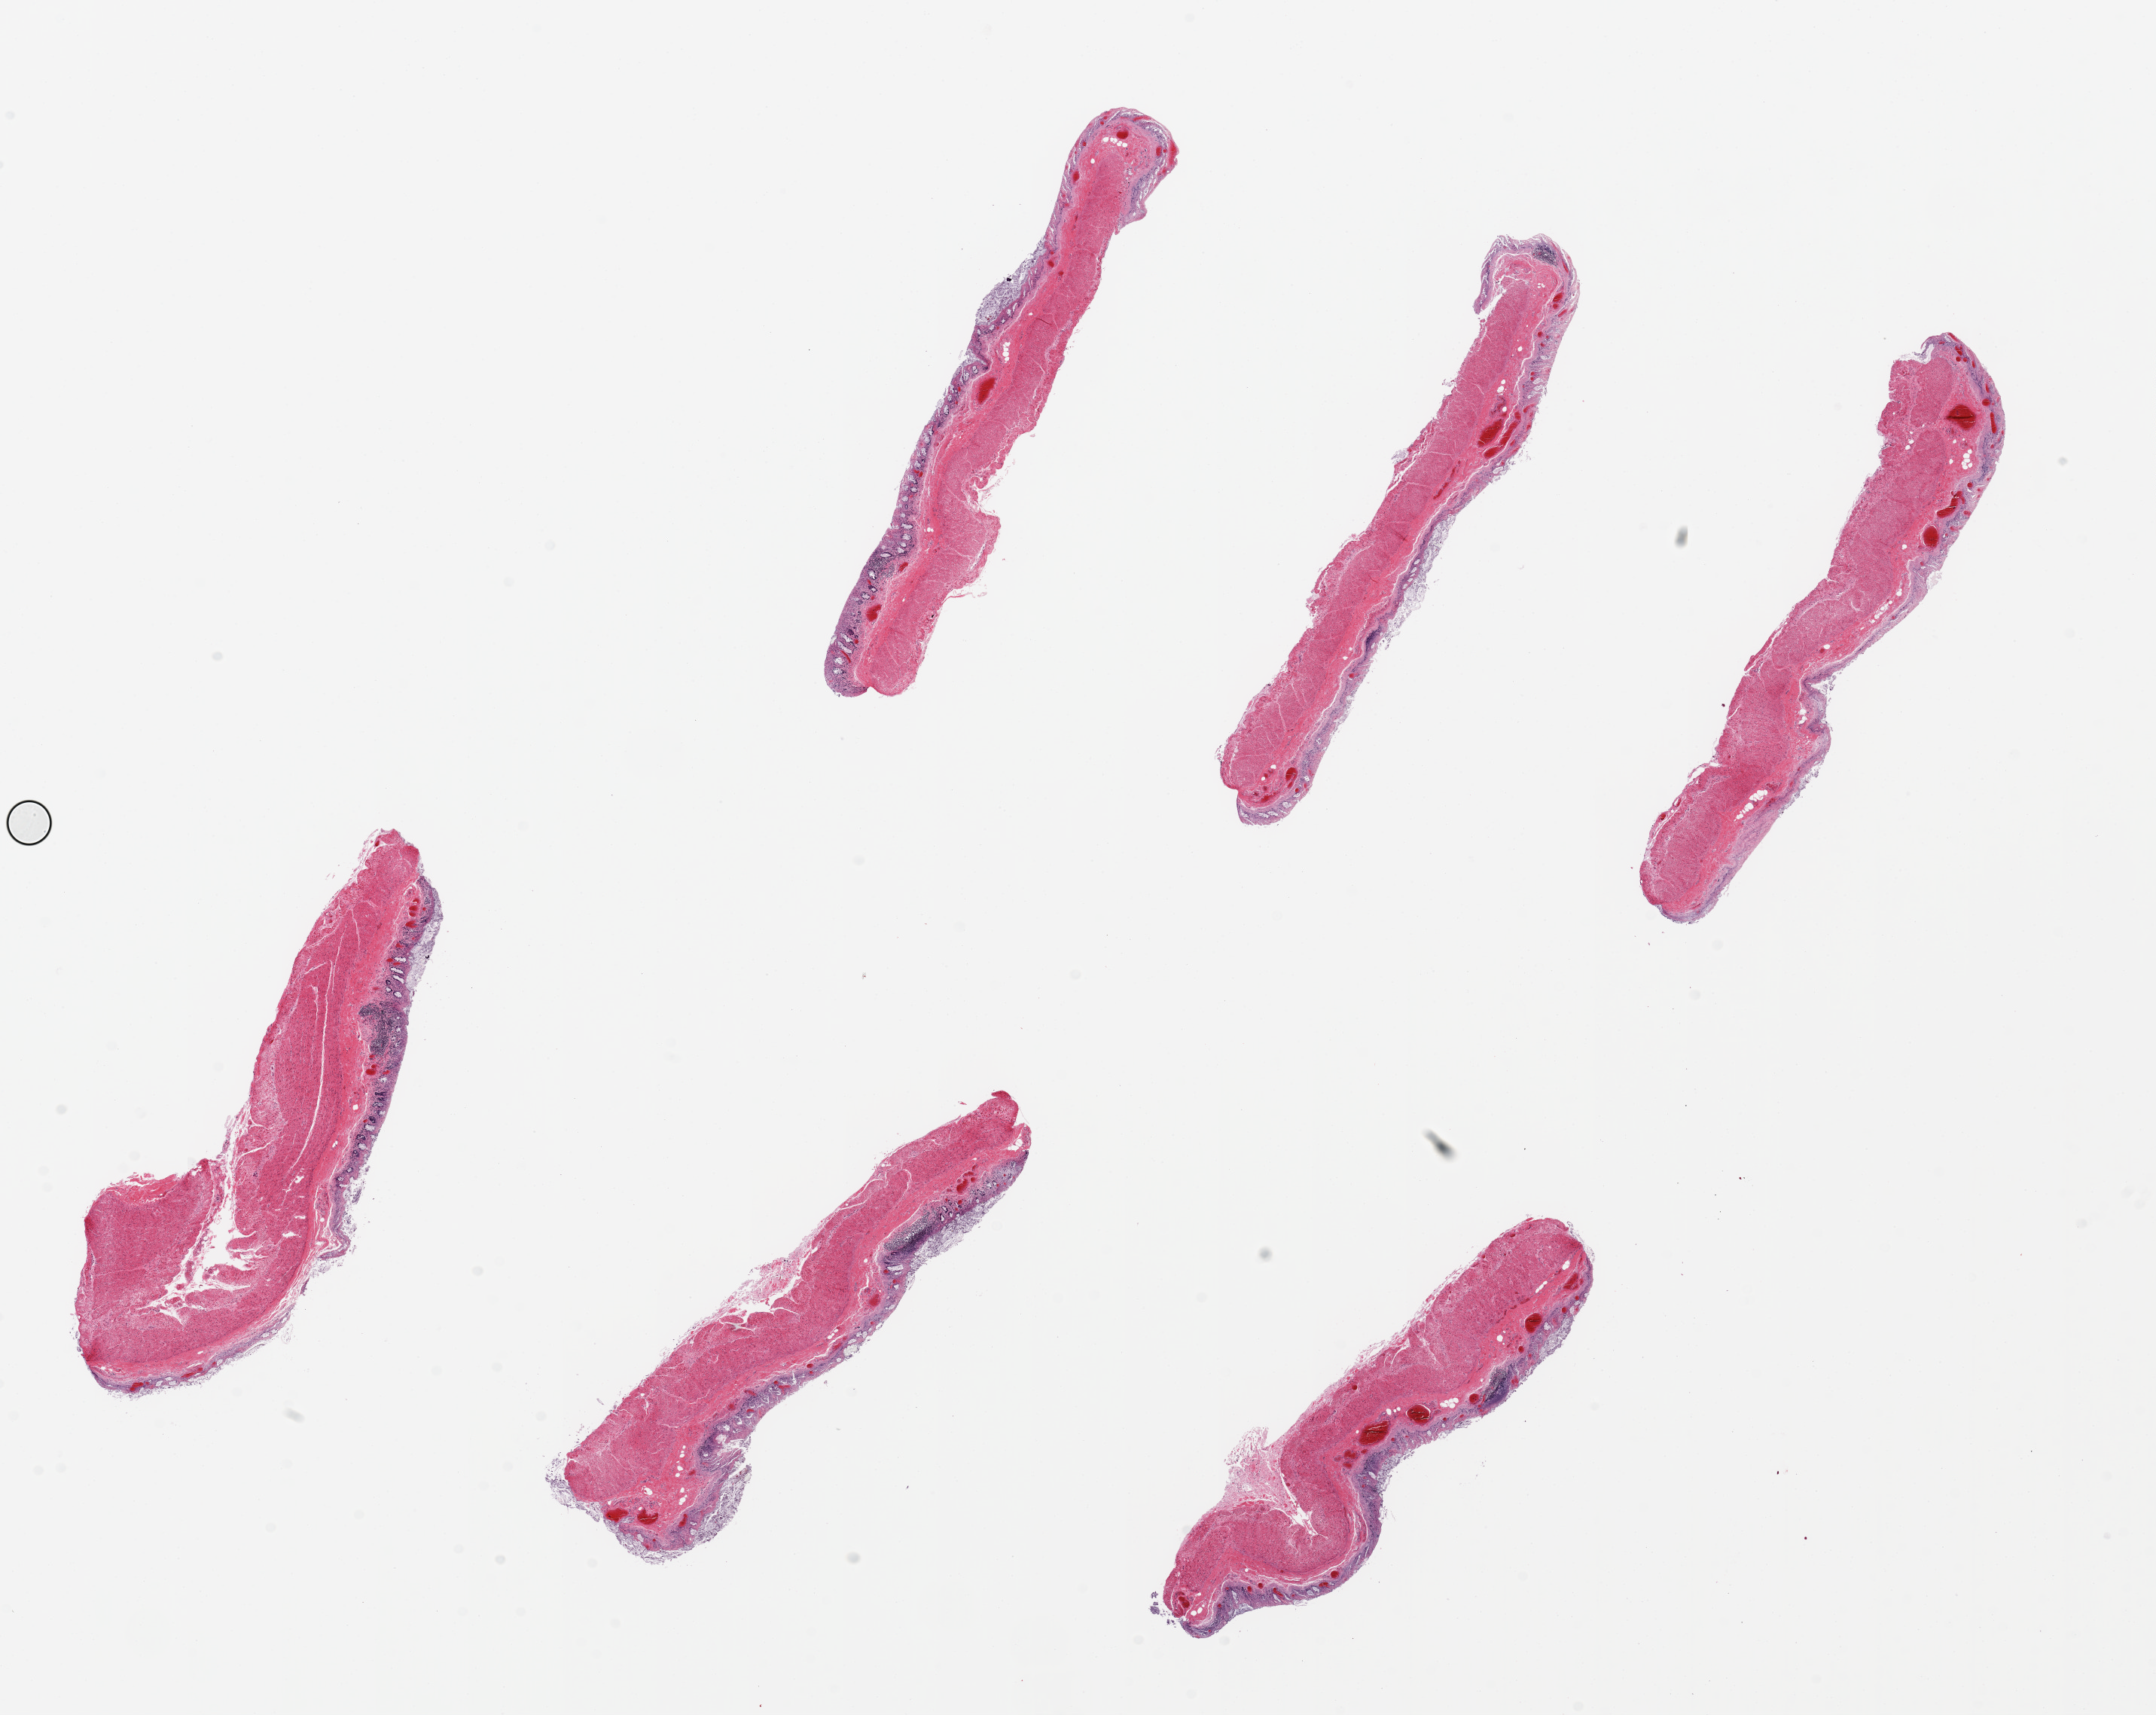
Hematoxylin and eosin (H&E) whole-slide image, low-resolution overview of the scanned area, about 22.6 x 18.0 mm. PAXgene-fixed, paraffin-embedded tissue. Target tissue: transverse colon. Tissue donor sample. Female donor.
* pathologist's review note for this sample: 6 pieces ~7x1mm, mucosa completely autolzyed,sloughing